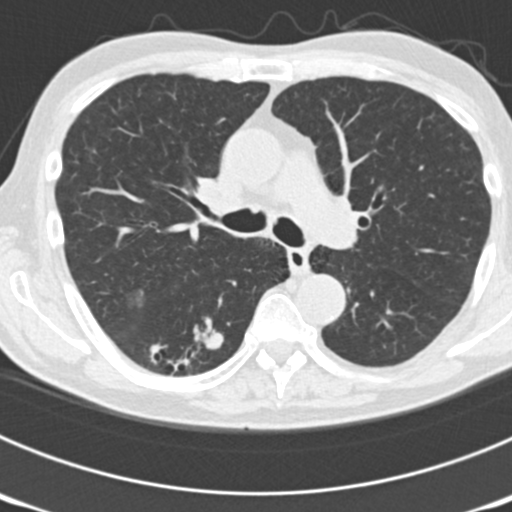
Low-dose screening chest CT, one axial slice; slice 116 of 177 in the series (ordered by position); lung window (W 1500 / L -600 HU); 2 mm slice thickness; 512 × 512 image matrix, field of view 300 × 300 mm.
Outlined on this slice (manually delineated by an expert):
- lesion 6 (nodule, lower lobe of right lung): bounding box (x1, y1, x2, y2) in pixels: (205, 331, 223, 350)